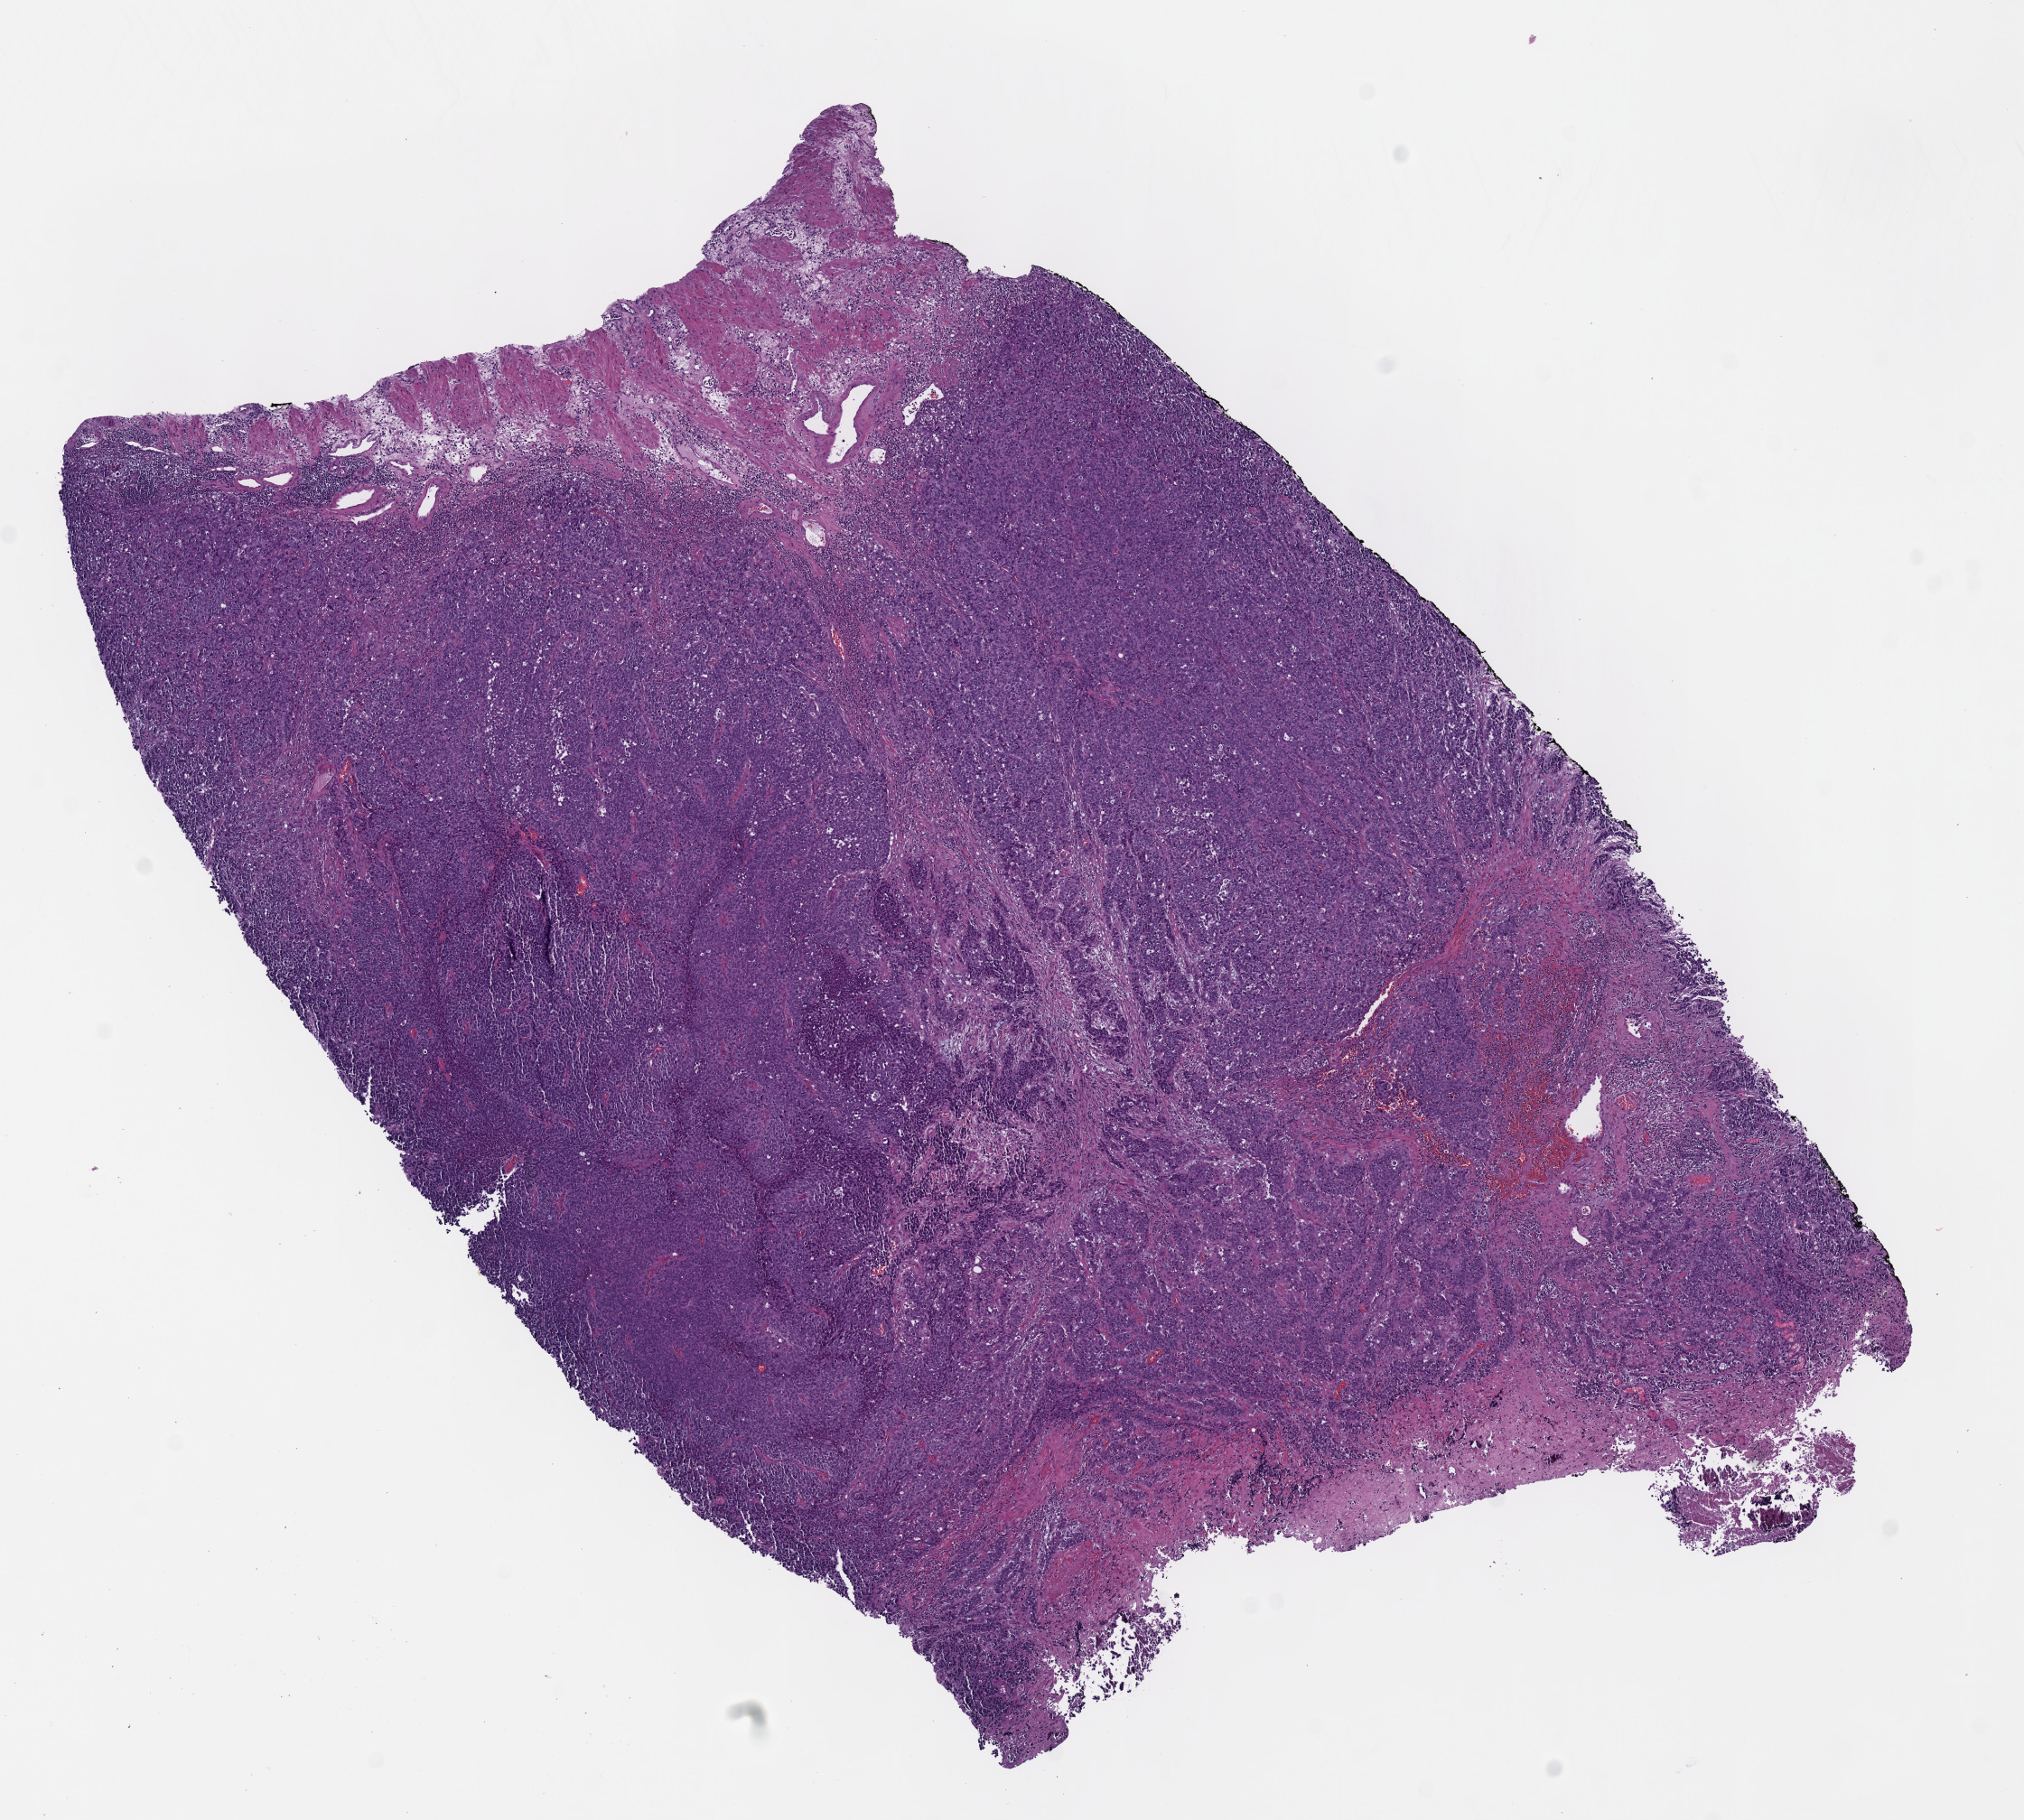
Whole-slide histology image, H&E, low-resolution overview of the scanned area, about 8.8 x 7.9 mm (from a 40x scan); formalin-fixed paraffin-embedded (FFPE) diagnostic section; bladder, primary tumour sample. Male patient; age at initial diagnosis 54 years. Histologic grade: high grade.
AJCC pathologic stage: III (7th edition). Lymph nodes positive (case pathology): 0 of 9 examined. TNM: T3b N0 M0. Diagnosis: Transitional cell carcinoma.